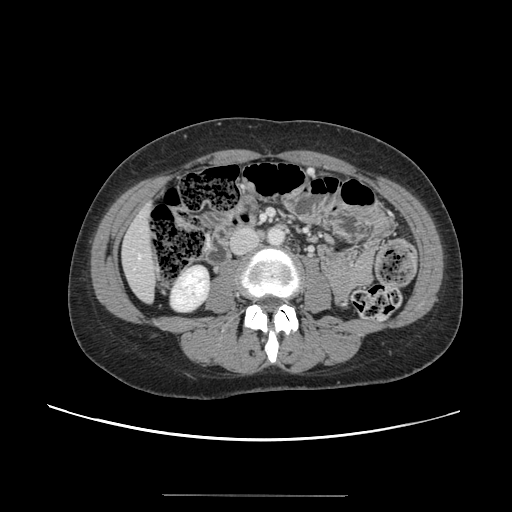
Contrast-enhanced abdominal CT, one axial slice; position 28 of 144 along the scan axis; 120 kVp; soft-tissue window (W 400 / L 40 HU); 512 × 512 image matrix. Female patient, age 53 years. Case-level facts recorded for this patient, not image findings: diagnosis: colorectal cancer liver metastases, imaged before liver resection.
Outlined on this slice (expert manual segmentation):
- liver: box from (x=124, y=207) to (x=157, y=301) px
- planned liver remnant (the part of the liver to remain after resection): (x=123, y=207)–(x=156, y=301)